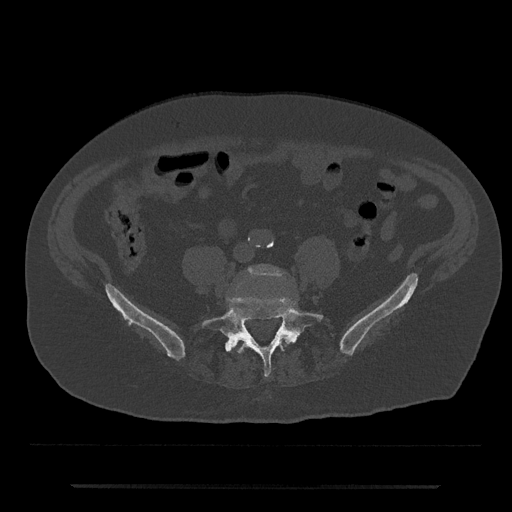
CT including the spine, one axial slice; slice 301 of 797 in the series (ordered by position); reconstruction kernel Br40s/3; bone window (W 1800 / L 400 HU); 0.5 mm slice thickness; 512 × 512 image matrix. Patient: male, 80 years. Case-level facts recorded for this patient, not image findings: primary cancer: prostate; vertebrae with lytic lesions (as recorded): L1, T11.
Structures marked on this image (semi-automatic segmentation, software-assisted and operator-edited):
- L4 vertebra: bounding box <247,265,284,279> (left, top, right, bottom; pixels)
- L5 vertebra: <201,296,323,377>